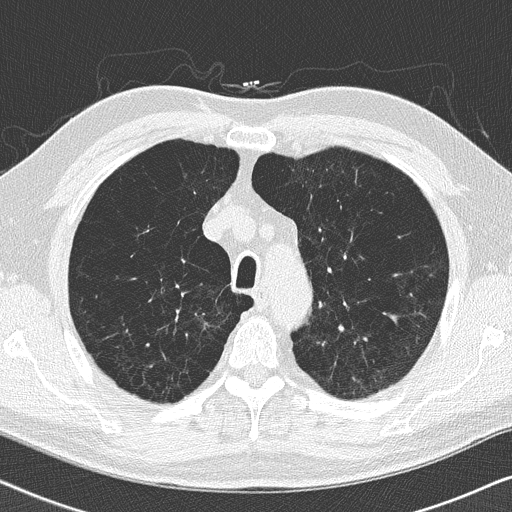
Chest CT (low-dose screening protocol), one axial image. Second annual screen. Lung window (W 1500 / L -600 HU). Slice 37 of 175 in the series. 512 × 512 image matrix, field of view 330 × 330 mm. Male, age 62 years at enrolment. Former smoker at enrolment.
Expert reader's lesion annotation, bounding box [x1, y1, x2, y2] px = [228, 264, 283, 317]. Reader record for this screening exam (exam-level; its link to the box is not recorded): non-calcified nodule or mass ≥4 mm, left upper lobe, 10 × 10 mm, soft tissue attenuation, pre-existing on the prior screen: yes; interval growth: no. Note: the box lies in the patient's right hemithorax on this image, whereas the reader's record names the left lung; they may be different findings. Participant outcome: lung cancer diagnosed 219 days after this screen — adenocarcinoma, NOS, left upper lobe, moderately differentiated (G2), stage IA (AJCC 6th edition), 10 mm at pathology.